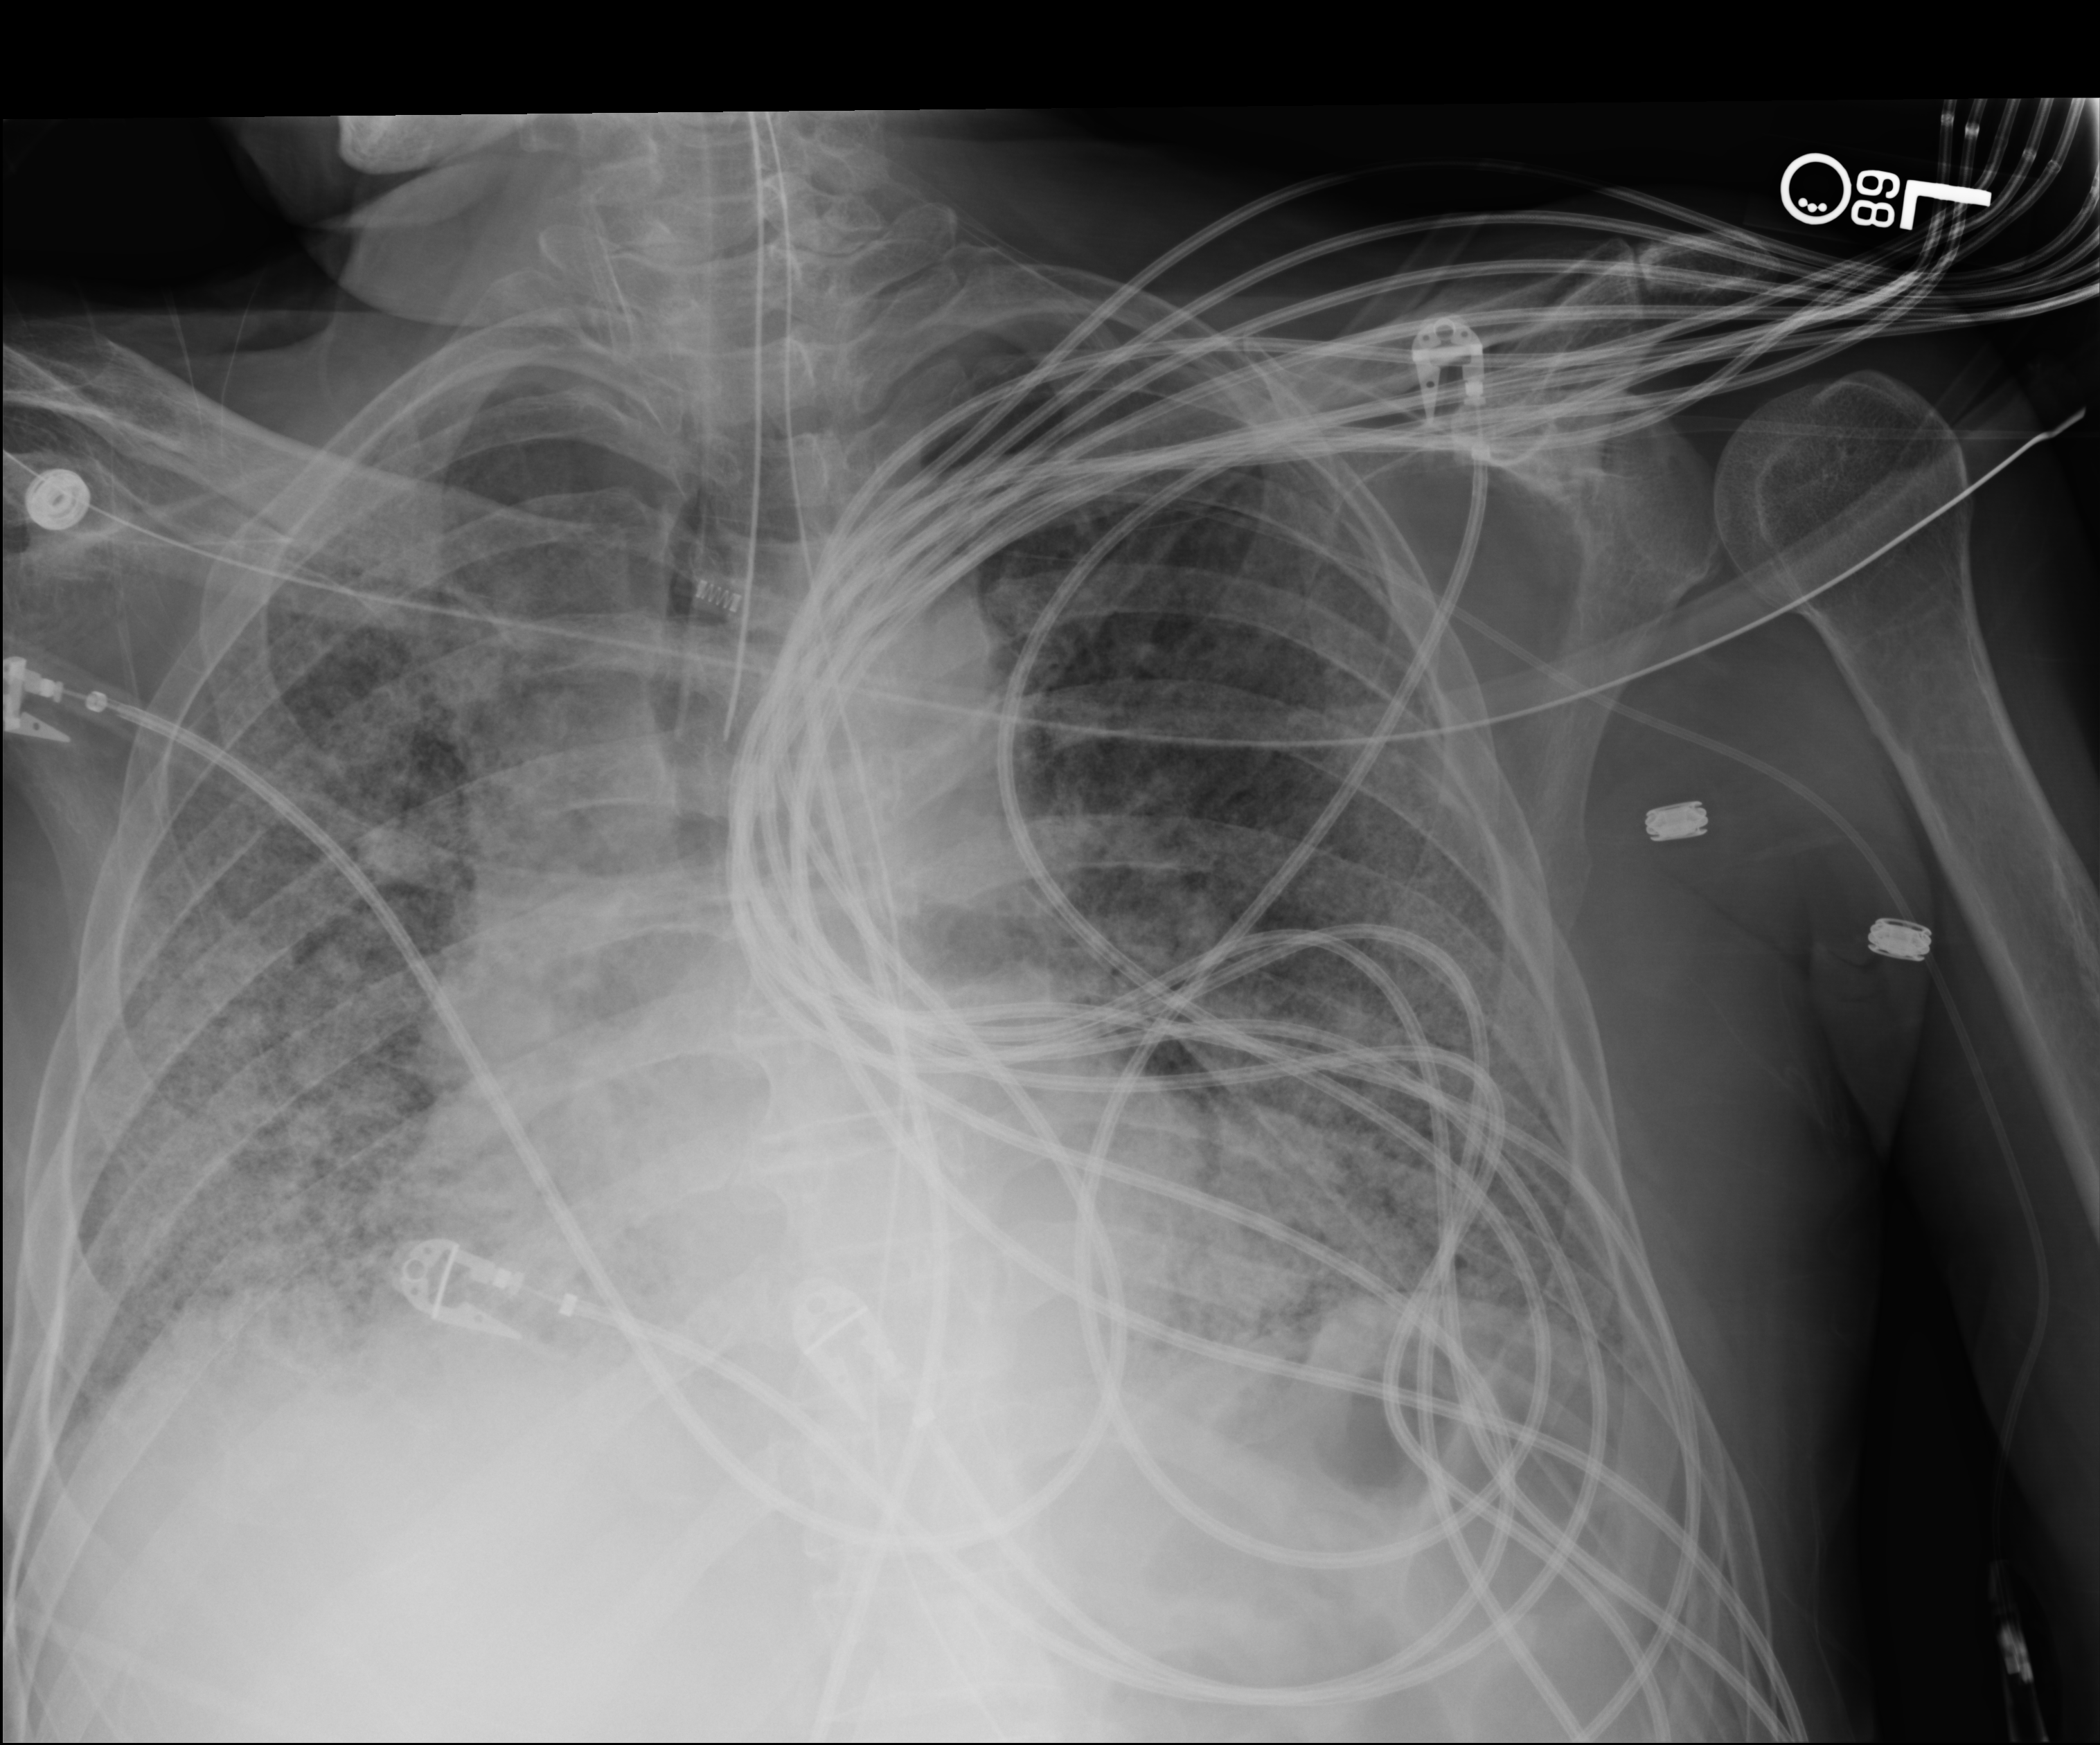
Chest X-ray (portable), anteroposterior (AP) projection. Patient hospitalised with COVID-19; male, aged 60–74 years.
From the hospital-stay record, not from the radiograph (when in the stay this image was taken is not recorded):
- admitted to intensive care during this hospital stay: yes